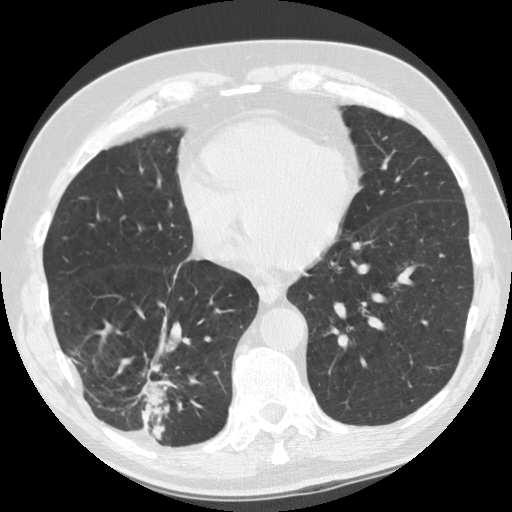
Low-dose screening chest CT, one axial slice; position 40 of 135 along the scan axis; lung window (W 1500 / L -600 HU); 2.5 mm slice thickness; 512 × 512 image matrix, field of view 340 × 340 mm.
Outlined on this slice (manually delineated by an expert):
- lesion 1 (tumor, lower lobe of right lung): bounding box (x1, y1, x2, y2) in pixels: (139, 378, 170, 440)